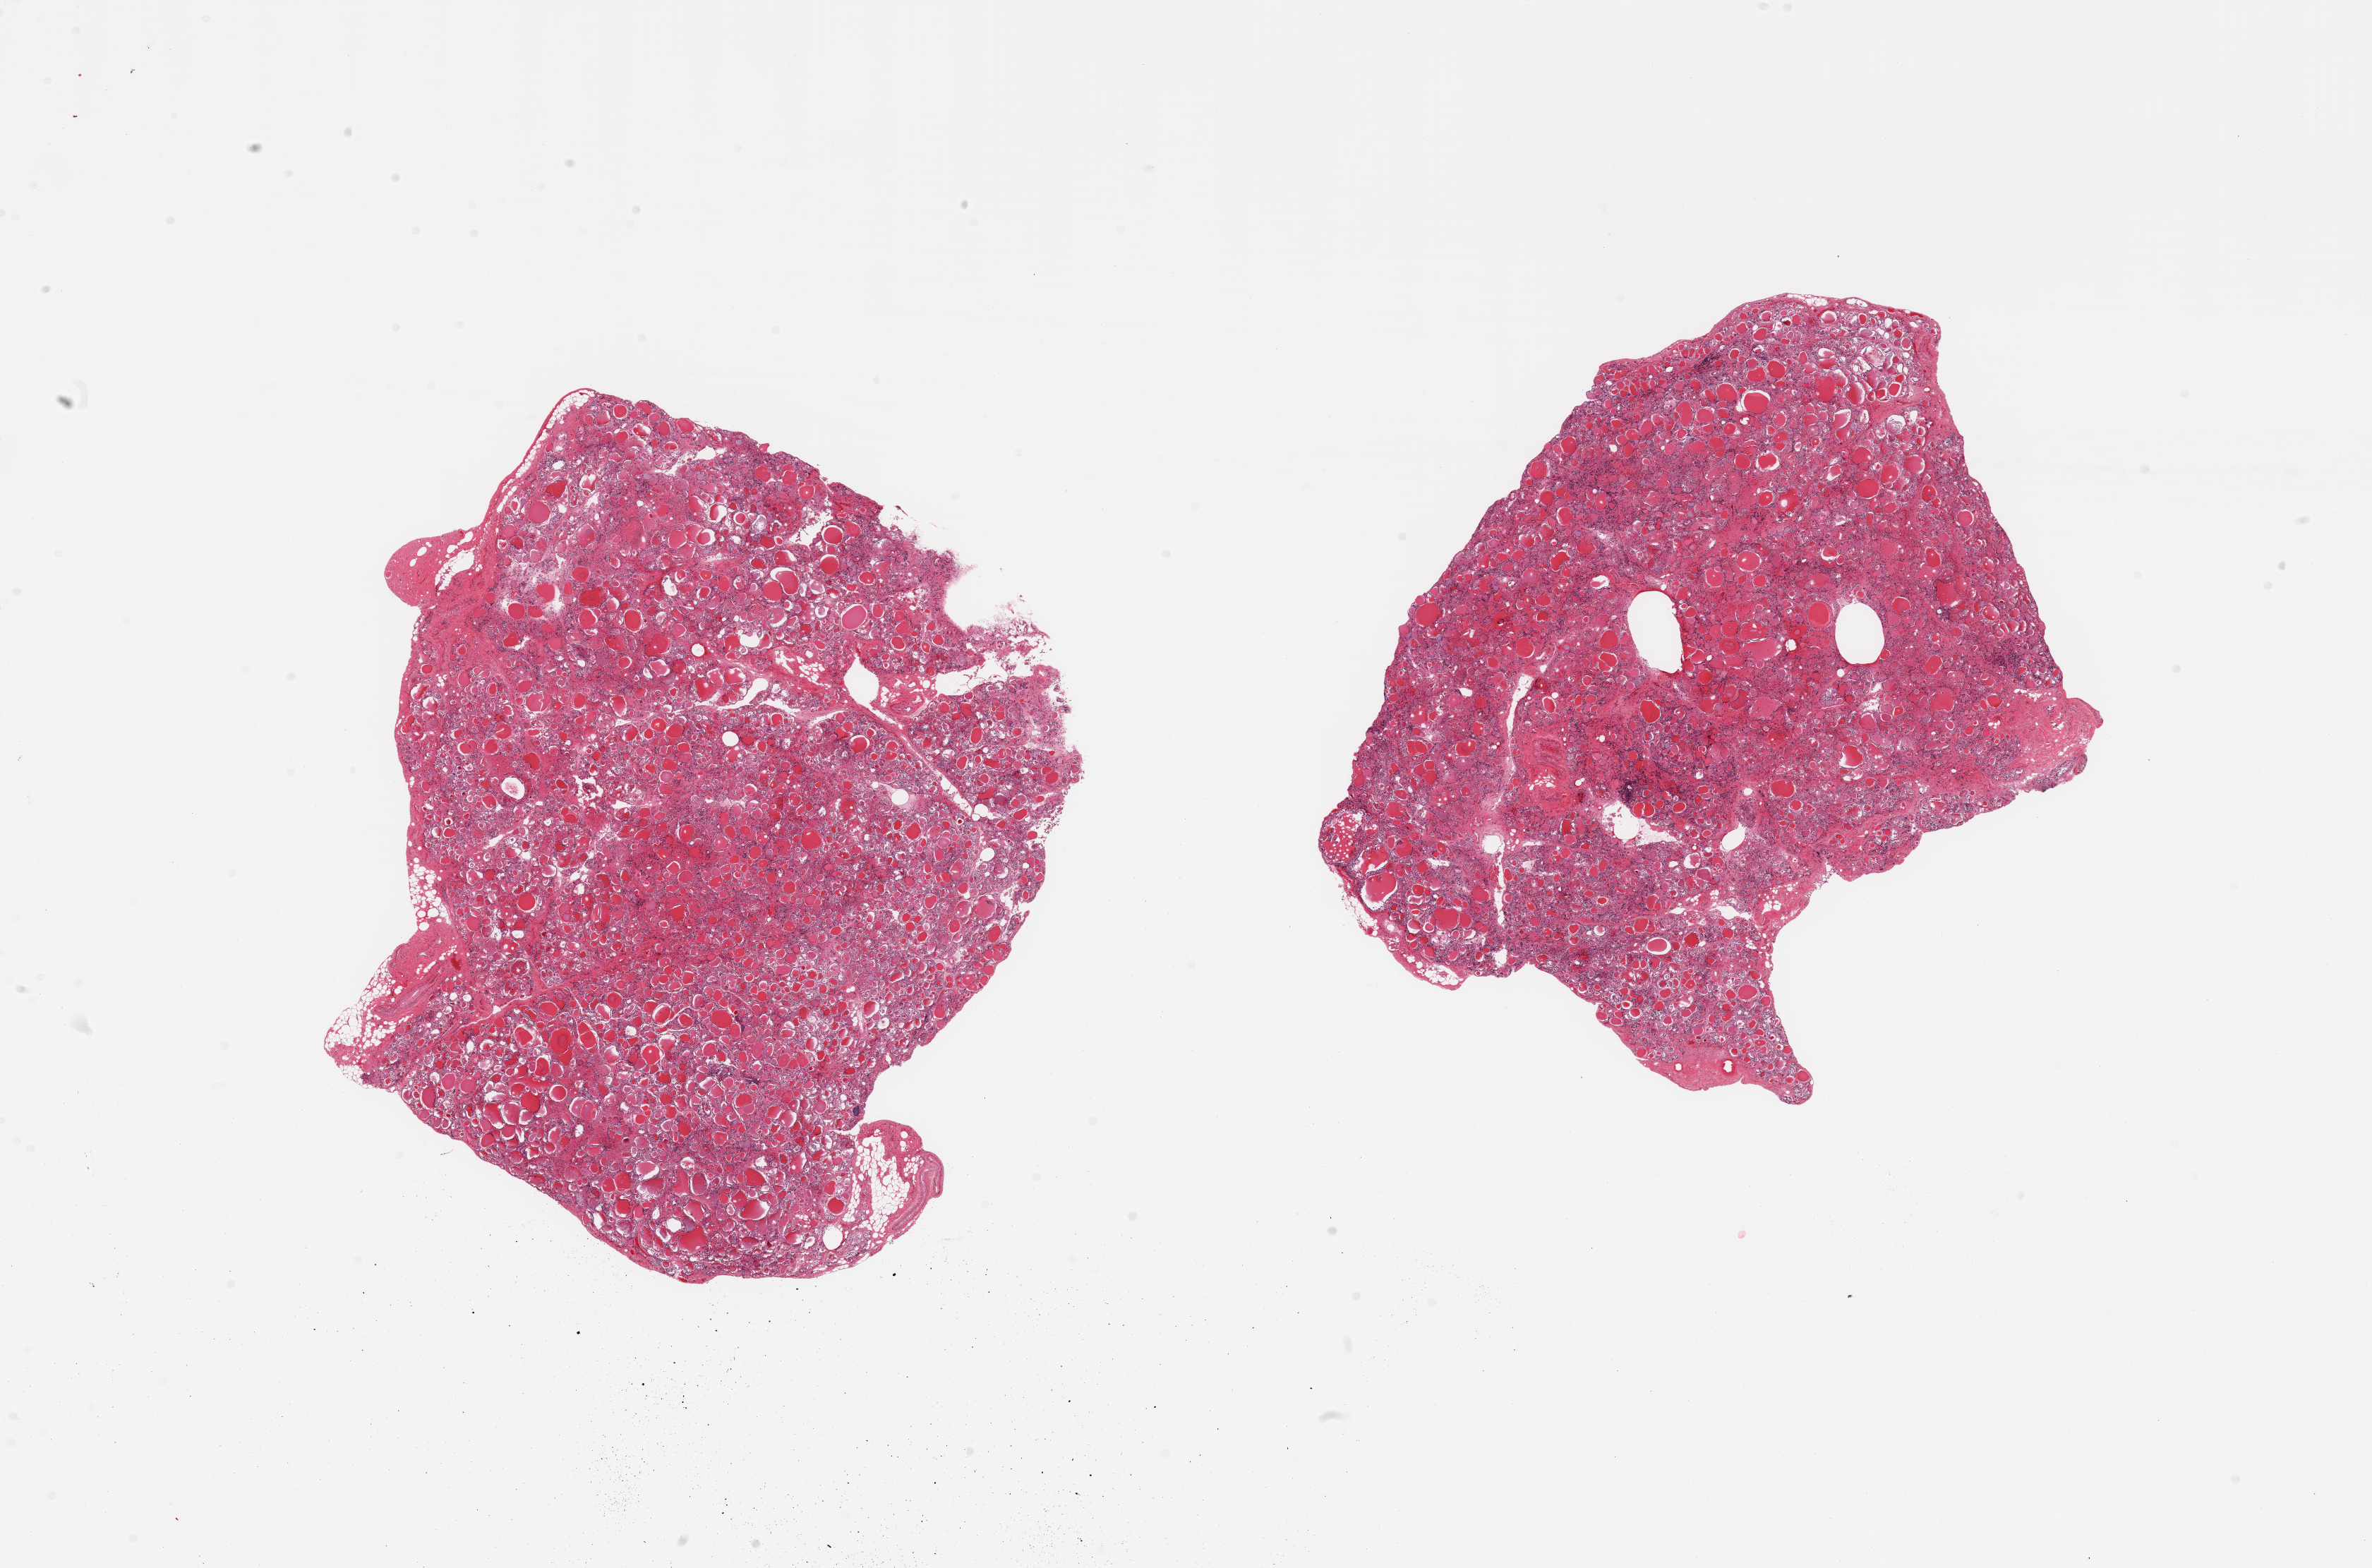
Whole-slide image, H&E stain, low-resolution overview of the scanned area, about 26.6 x 17.6 mm, PAXgene-fixed paraffin-embedded (PFPE) section, sampled site (target tissue): thyroid, tissue donor sample. Donor: female.
Reviewer comment on this tissue sample: 2 pieces, no abnormalities.